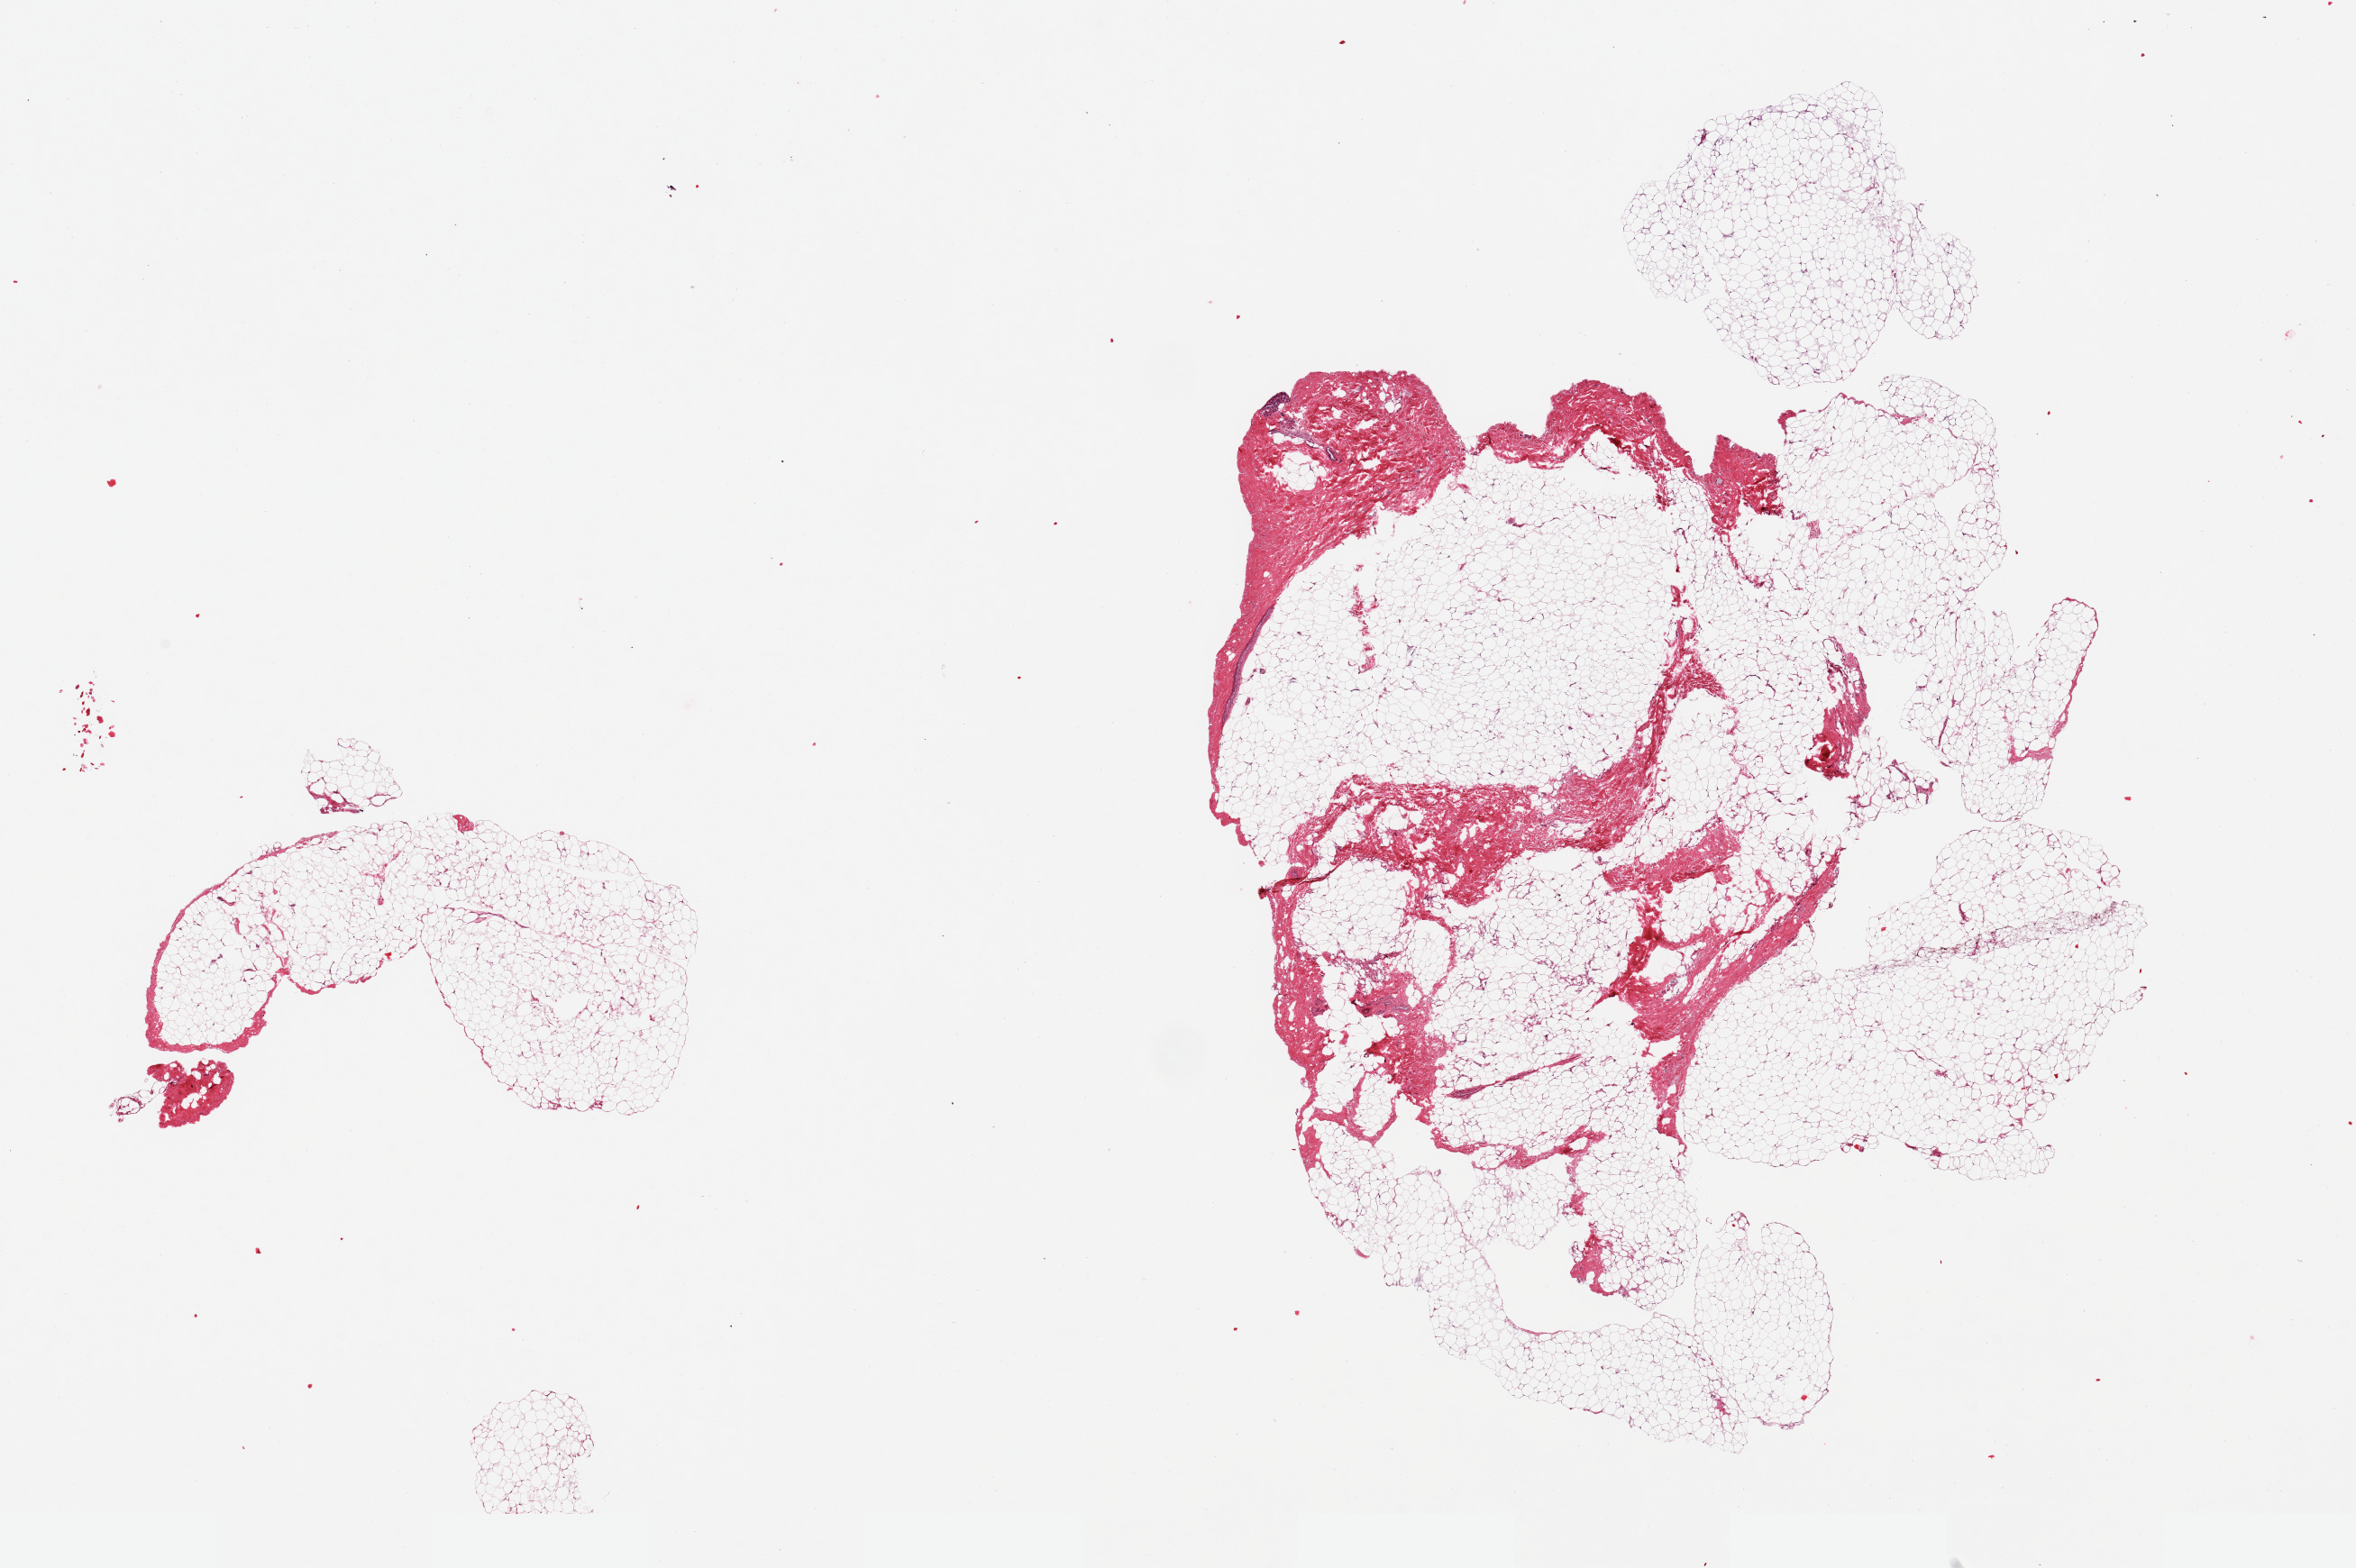
H&E whole-slide image, brightfield, shown as a low-resolution overview of the whole scanned area (about 20.7 x 13.8 mm, from a 20x scan); PAXgene-fixed paraffin-embedded (PFPE) section; target tissue: breast; tissue donor sample. Male donor.
• reviewer comment on this tissue sample: 2 pieces; mostly fat with some fibrovascular component and a few glandular structures at one edge